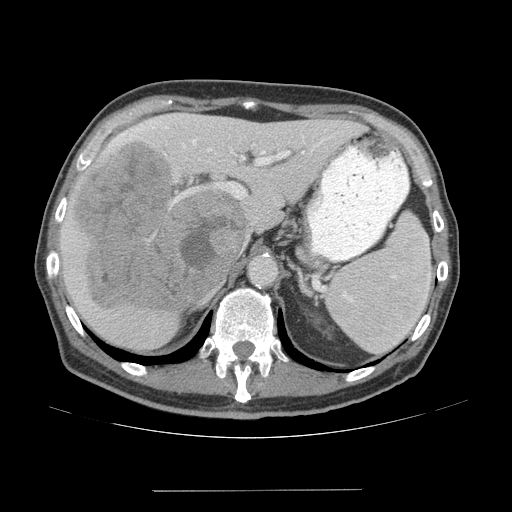
Contrast-enhanced abdominal CT (liver protocol), one axial slice; slice 41 of 77 in the series (ordered by position); reconstruction kernel STANDARD; 140 kVp; soft-tissue window (W 400 / L 40 HU); 512 × 512 image matrix, field of view 400 × 400 mm. From the clinical record (not read from this slice): diagnosis: hepatocellular carcinoma (patient treated with transarterial chemoembolisation; whether this scan precedes or follows treatment is not stated here); TNM stage (as recorded): Stage-IVA; Child-Pugh class: A; tumour nodularity: uninodular.
Outlined on this slice (semi-automatically segmented with operator editing):
- liver parenchyma outside the tumour (the mass and vessels are separate outlines, so this box may not span the whole liver): bounding box (x1, y1, x2, y2) in pixels: (60, 112, 364, 350)
- mass: (72, 142, 249, 314)
- liver vessels: (109, 115, 324, 205)